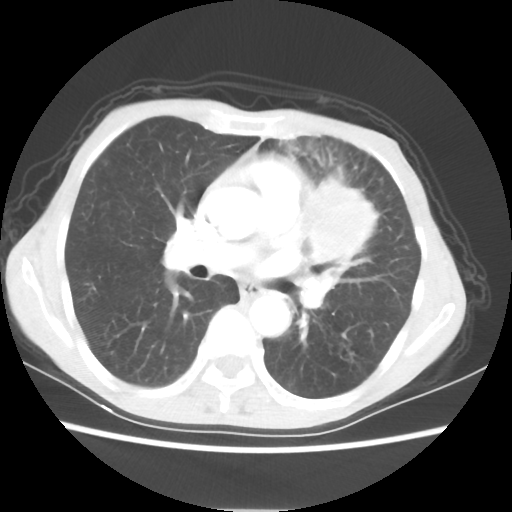
Chest CT, one axial slice; position 32 of 56 along the scan axis; reconstruction kernel STANDARD; 80 kVp; lung window (W 1500 / L -600 HU); 5 mm slice thickness; 512 × 512 image matrix. Patient: female, 60 years. From the clinical record (not read from this slice): clinical TNM (as recorded): T4 N1 M0.
Outlined on this slice (rectangle marked by the reading radiologist):
- lung tumour (recorded histology: adenocarcinoma): bounding box (x1, y1, x2, y2) in pixels: (306, 180, 380, 268)